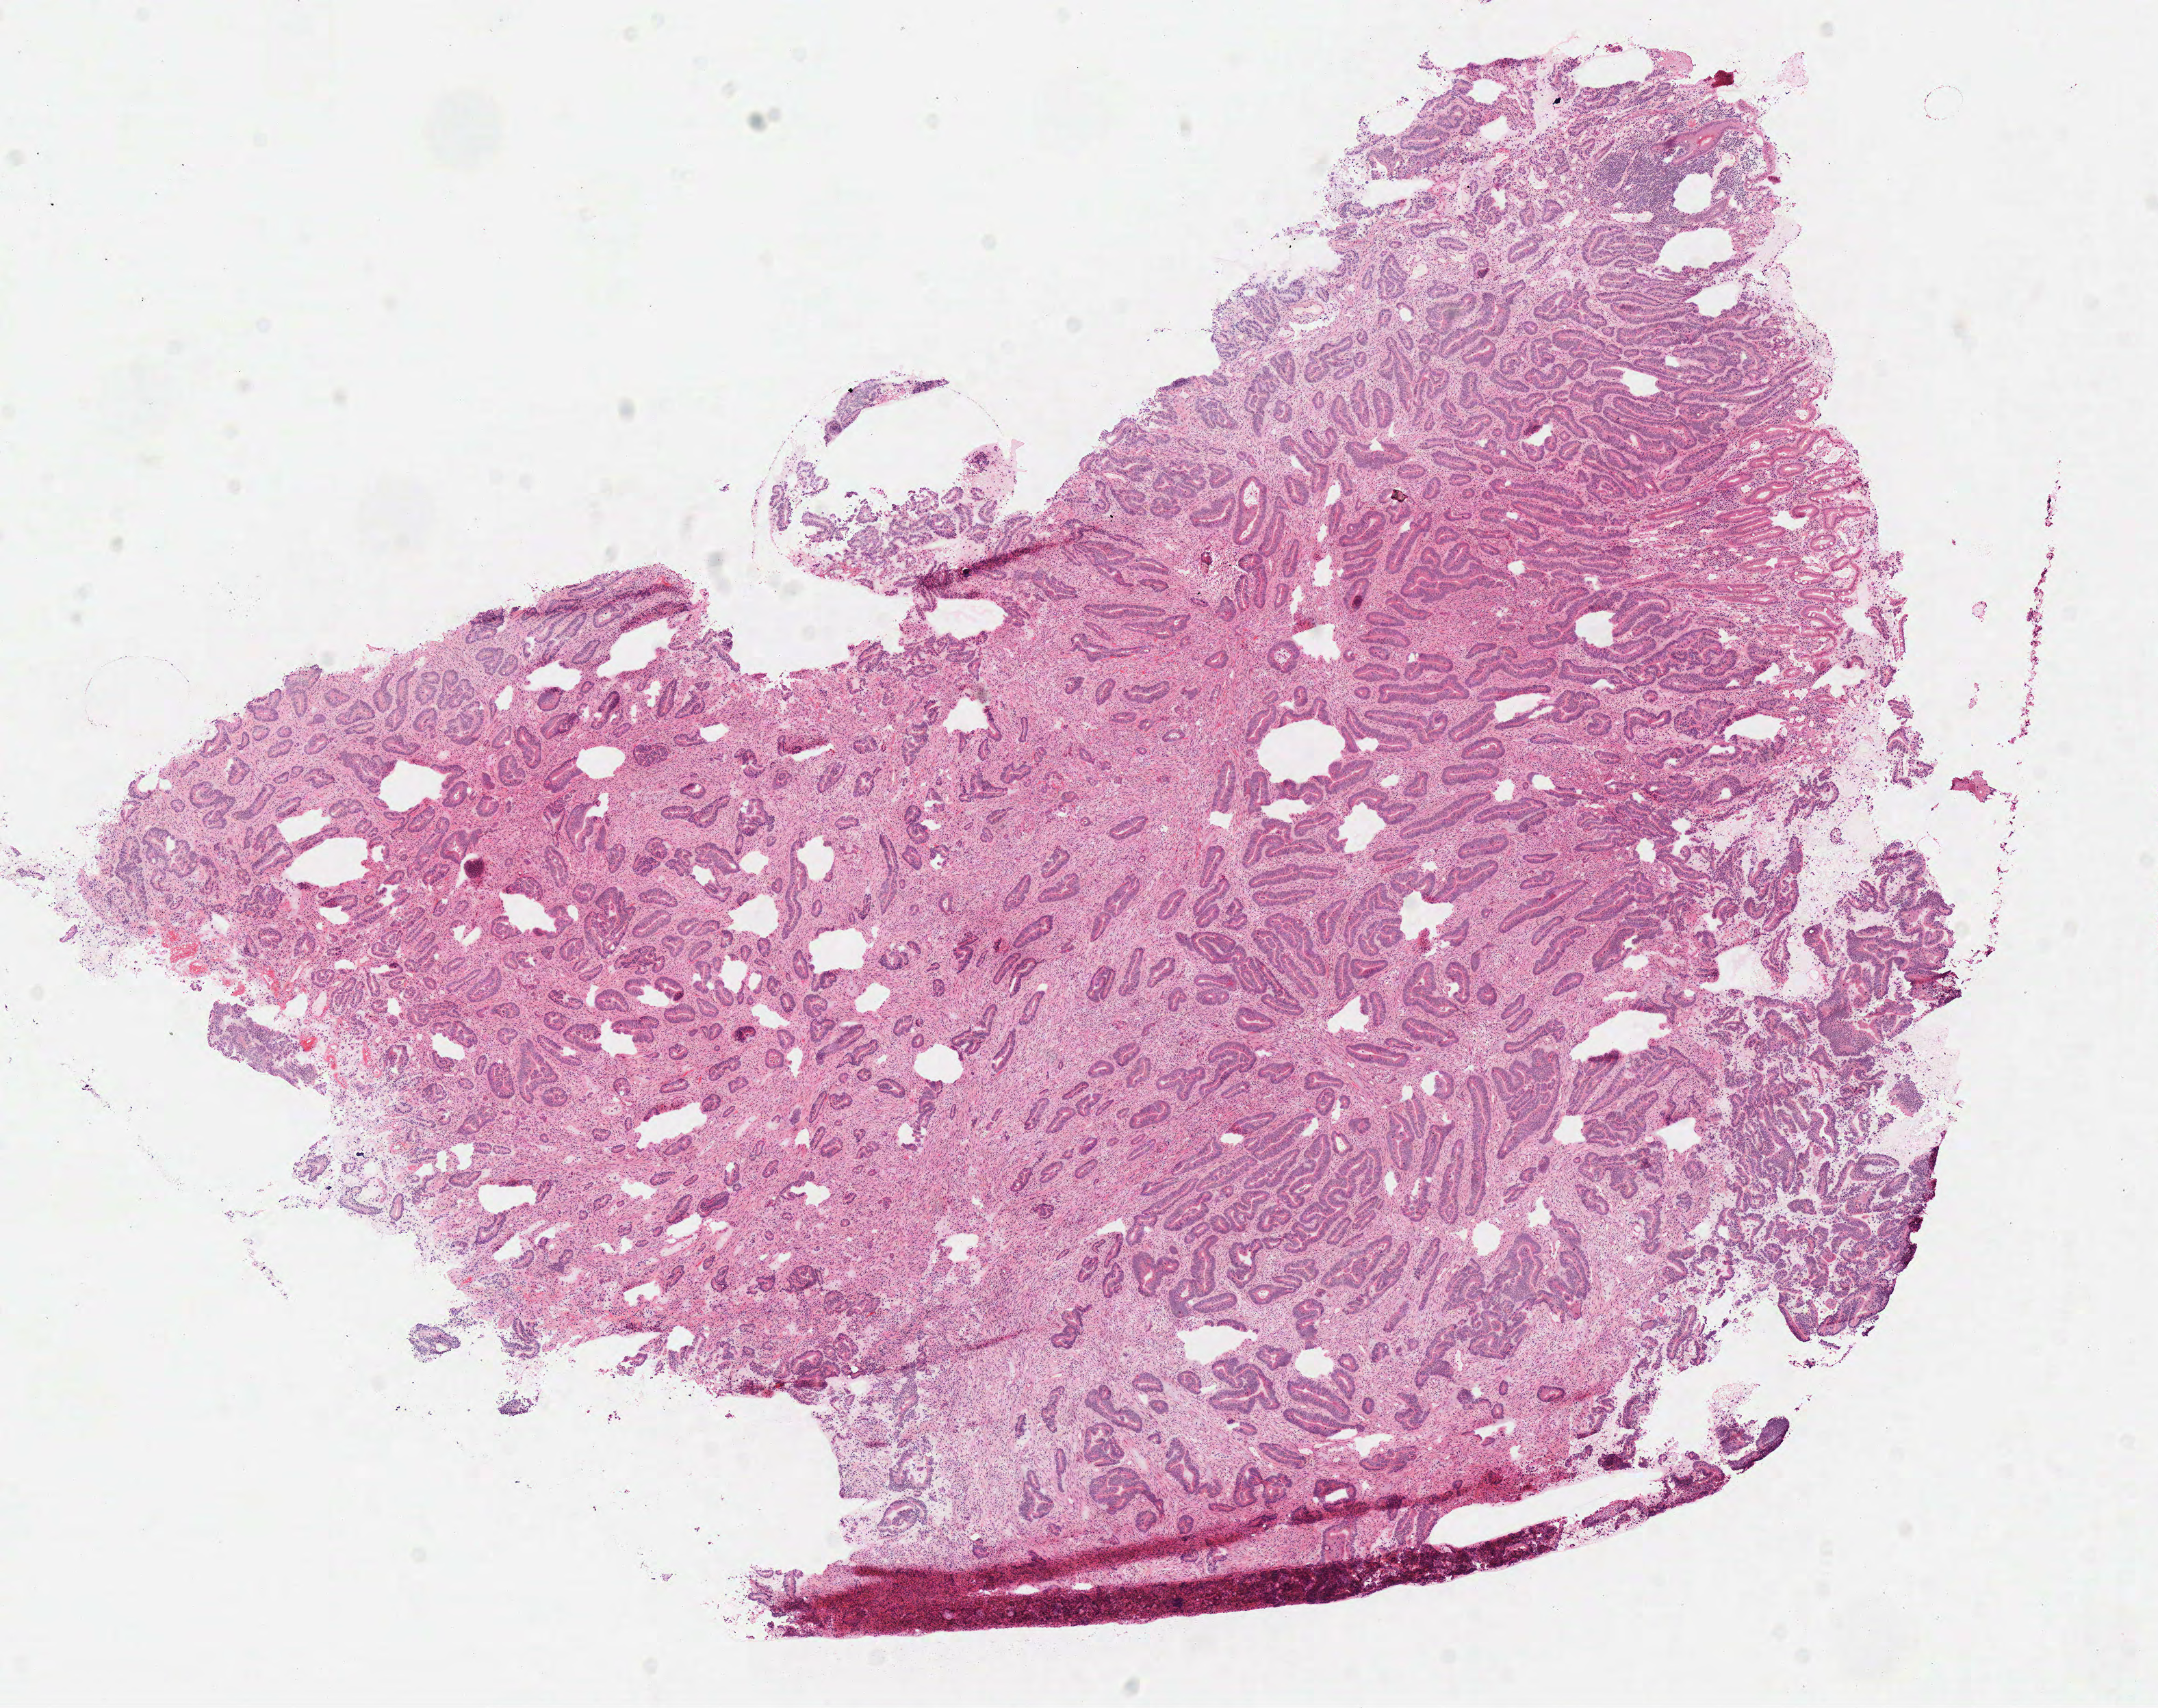
H&E-stained whole-slide image — shown as a low-resolution overview of the whole scanned area (about 12.4 x 9.8 mm, slide scanned at 40x); frozen section; sample: primary tumour, colon. Male, age 44 years at initial diagnosis. Composition of this section per pathologist review: tumour cells 99%, tumour nuclei 75%, normal cells 1%, stromal cells 0%, necrosis 0%. Infiltration values recorded for this section: lymphocyte infiltration 5%, monocyte infiltration 1%, neutrophil infiltration 2%.
AJCC pathologic stage: IIA. Lymph nodes positive (case pathology): 0 of 44 examined. Histologic diagnosis: Adenocarcinoma, NOS (ascending colon).